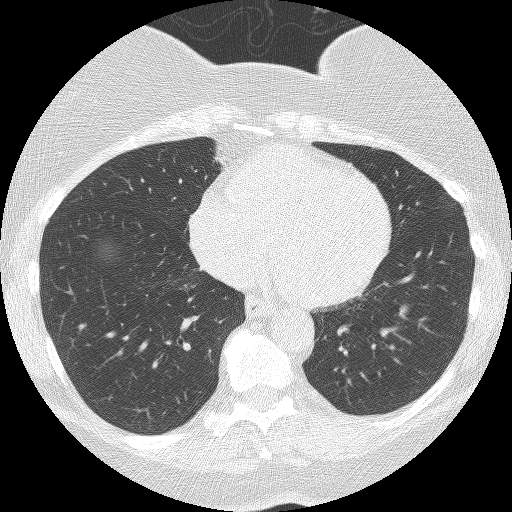
Axial slice from a low-dose chest CT screening exam, third annual screen, lung window (W 1500 / L -600 HU), 2.5 mm slice thickness. Female, age 55 years at enrolment. Former smoker at enrolment.
- Lesion marked by an expert reader, box from (x=382, y=287) to (x=431, y=335) px.
- The screening reader recorded 3 non-calcified nodules or masses ≥4 mm on this exam (right lower lobe, right lower lobe, left lower lobe); which of them this box marks is not recorded.
- Official screen result: positive, no significant change: stable abnormalities potentially related to lung cancer, unchanged since the prior screening exam.